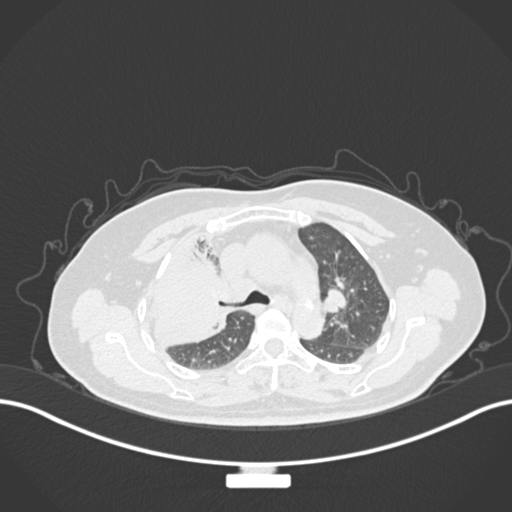
Chest CT, one axial slice. Slice 107 of 177 in the series (ordered by position). Reconstruction kernel B30f. 120 kVp. Lung window (W 1500 / L -600 HU). 1 mm slice thickness. 512 × 512 image matrix, field of view 400 × 400 mm. Female patient, age 60 years. Case-level facts recorded for this patient, not image findings: clinical TNM (as recorded): T3 N1 M1.
Outlined on this slice (bounding box drawn by a radiologist):
- lung tumour (recorded histology: adenocarcinoma): bounding box (x1, y1, x2, y2) in pixels: (149, 243, 233, 356)